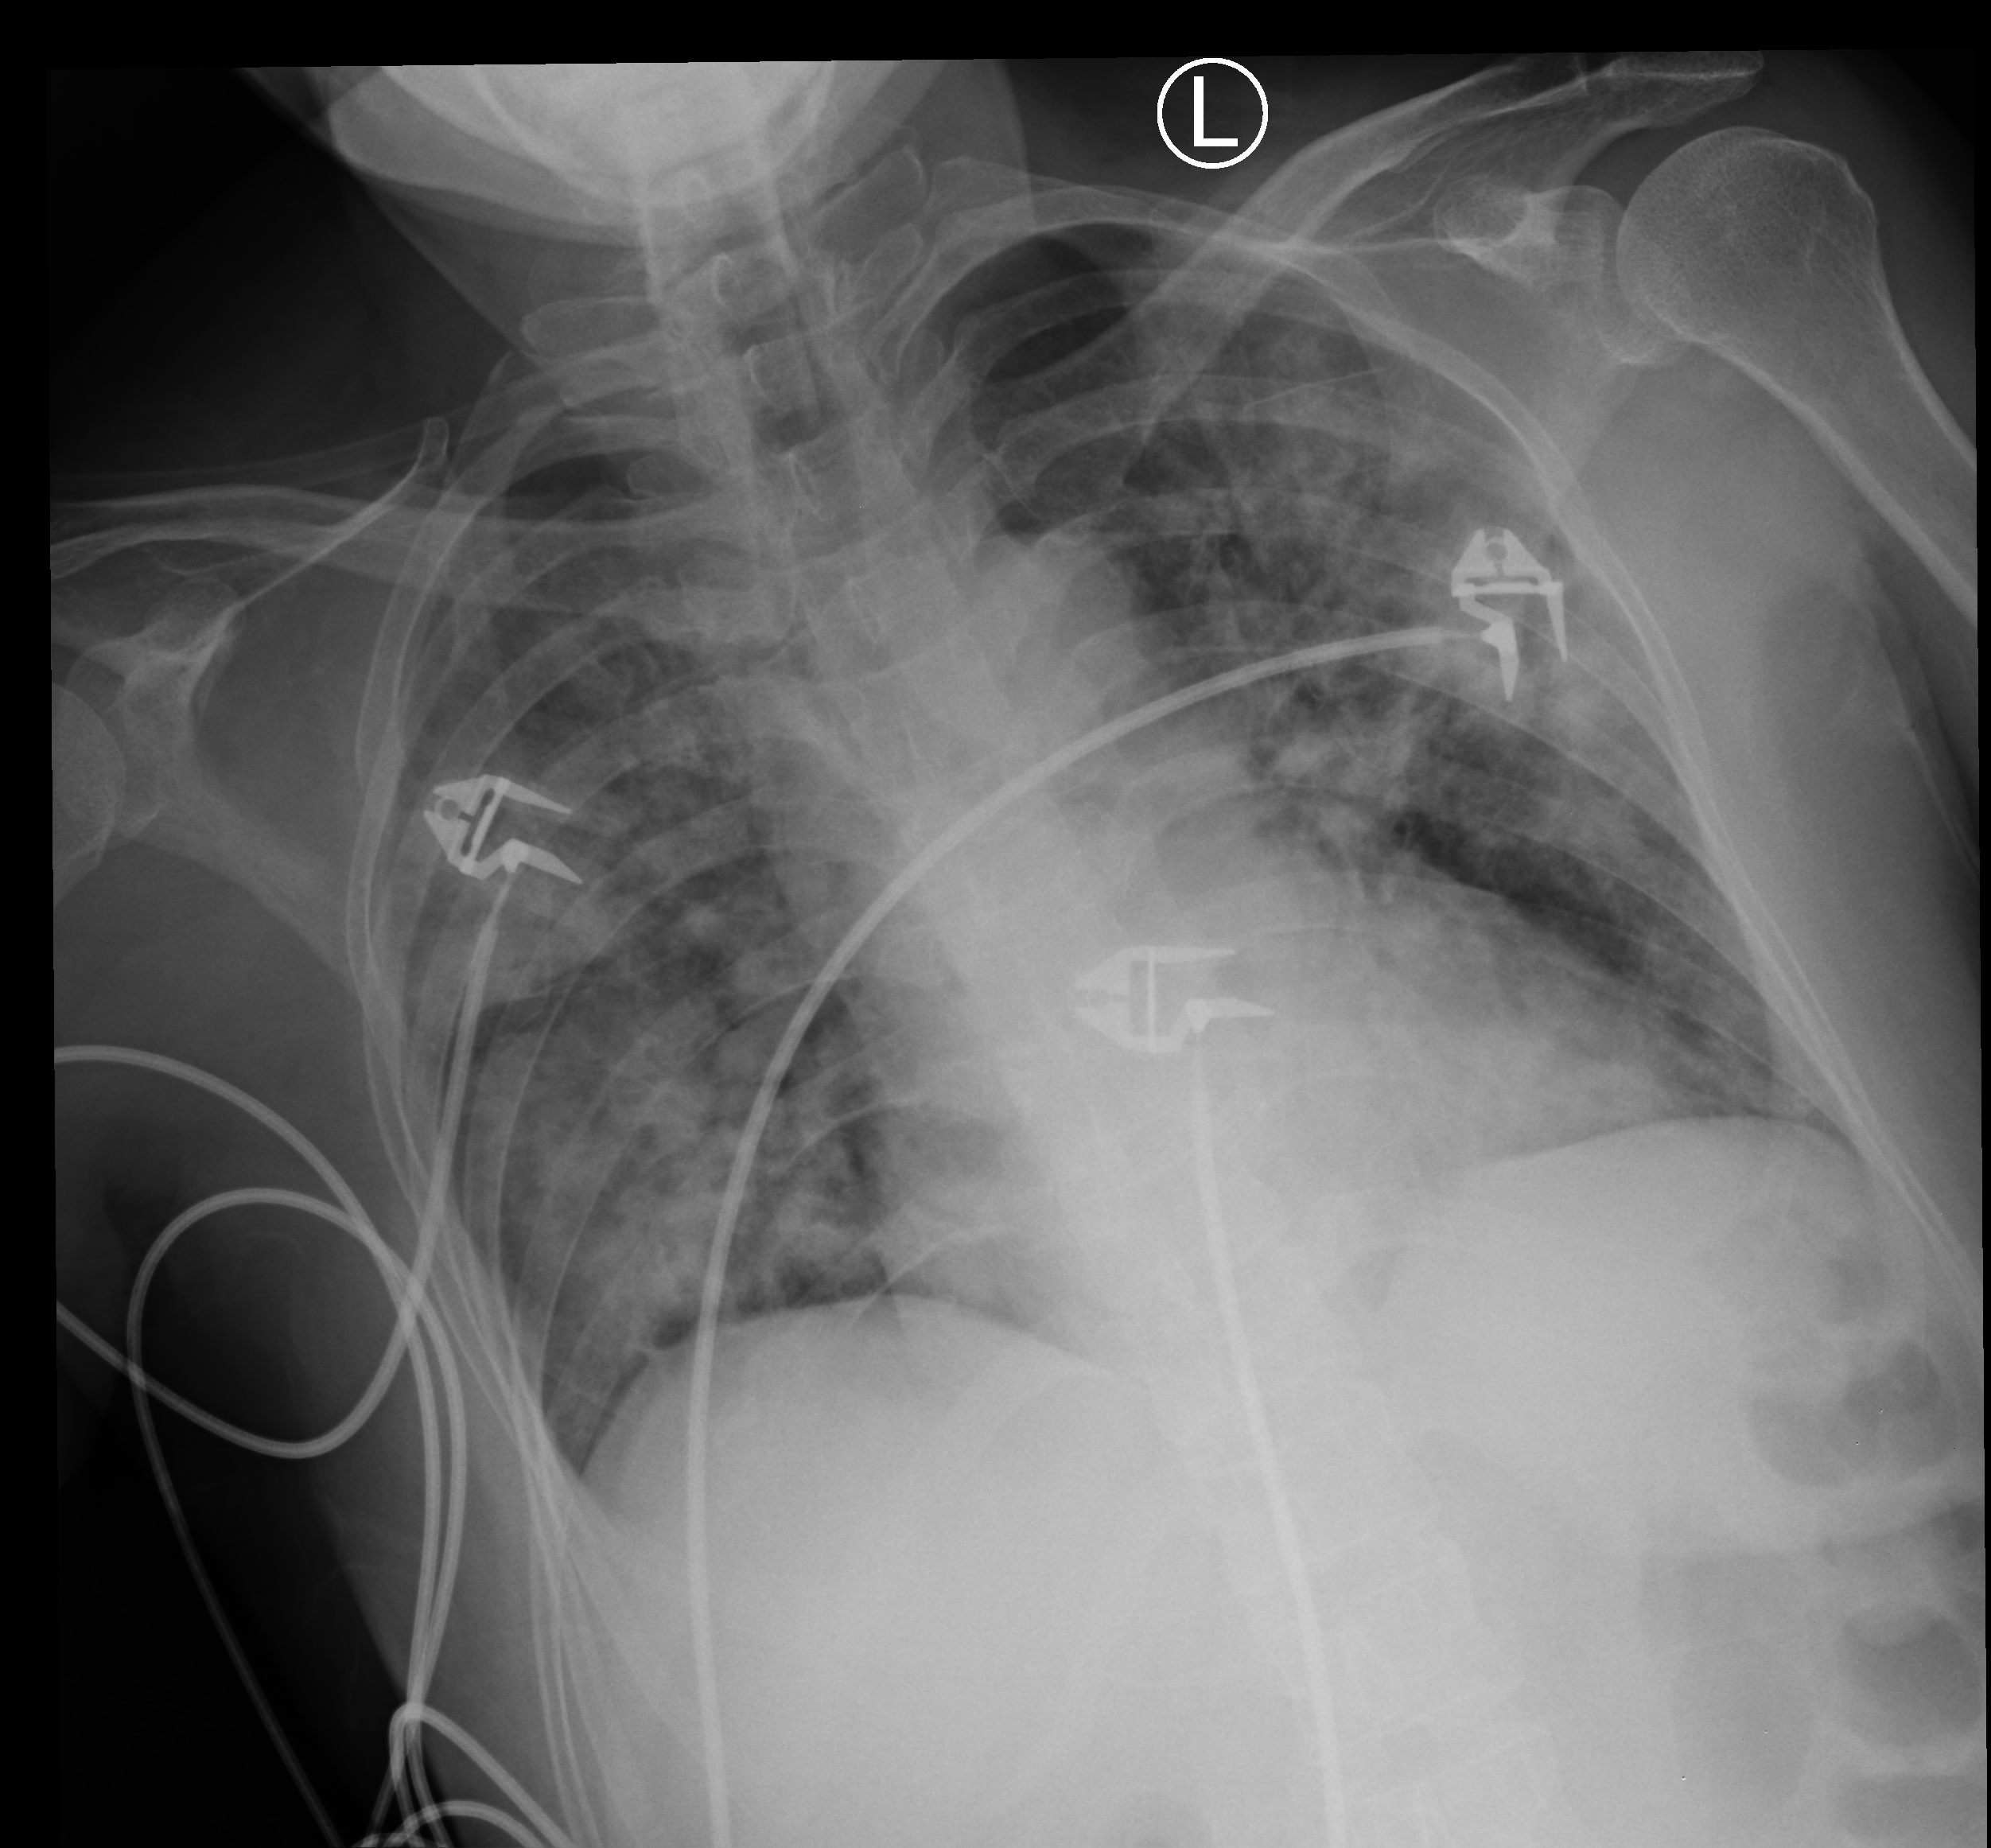
Bedside chest radiograph (computed radiography); anteroposterior (AP) projection. Patient hospitalised with COVID-19; female, aged 60–74 years.
Admission-level facts for this patient (not findings on this image; timing relative to this image not recorded): chronic kidney disease (admission record): no; other chronic lung disease (admission record): no; mechanically ventilated during this hospital stay: yes.